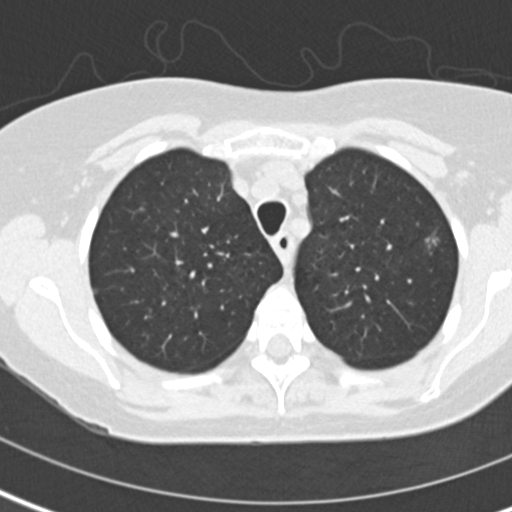
Axial slice from a low-dose chest CT screening exam, second screening round (one year after baseline), lung window (W 1500 / L -600 HU), 2 mm slice thickness, standard (soft-tissue) reconstruction kernel (B30f), 120 kVp, slice 30 of 141 in the series. Female participant, aged 60 years at enrolment.
- Lesion marked by an expert reader, bounding box (x1, y1, x2, y2) in pixels: (412, 223, 467, 263).
- The screening reader recorded 2 non-calcified nodules or masses ≥4 mm on this exam (left upper lobe, left upper lobe); which of them this box marks is not recorded.